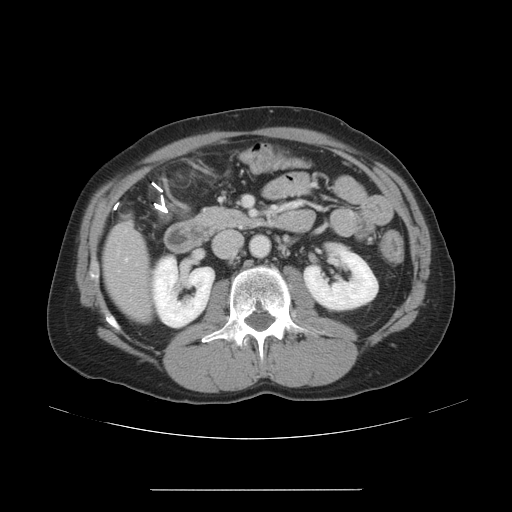
Contrast-enhanced abdominal CT, one axial slice. 120 kVp. Intravenous contrast given. Soft-tissue window (W 400 / L 40 HU). 5 mm slice thickness. 512 × 512 image matrix, field of view 409 × 409 mm. Male patient, age 56 years. From the clinical record (not read from this slice): diagnosis: colorectal cancer liver metastases, imaged before liver resection; multiple liver metastases: yes; largest metastasis: 1.8 cm; chemotherapy before resection: yes.
Annotated regions visible in this slice (outlined manually by an expert reader):
- hepatic veins: box from (x=124, y=257) to (x=129, y=263) px
- liver: (x=106, y=222)–(x=151, y=321)
- planned liver remnant (the part of the liver to remain after resection): (x=107, y=270)–(x=151, y=321)